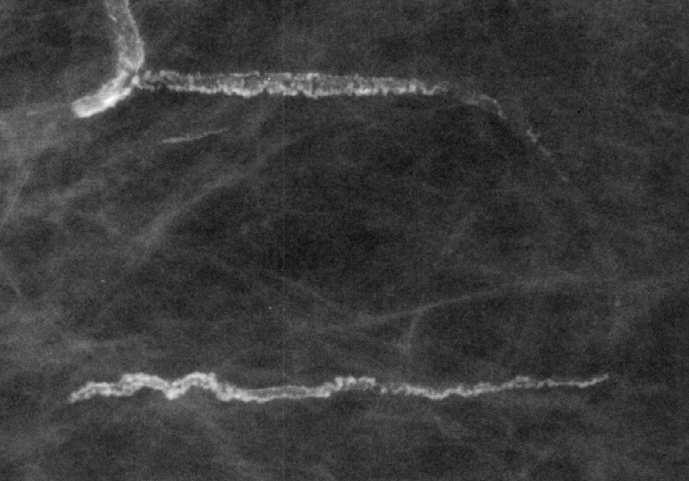
Region of interest cut from a scanned film mammogram (one marked finding); right breast; CC view.
- Marked abnormality: calcifications, morphology vascular; BI-RADS assessment category 2; subtlety rating 4 on a 1 (subtle) to 5 (obvious) scale; benign without callback (not worked up further).